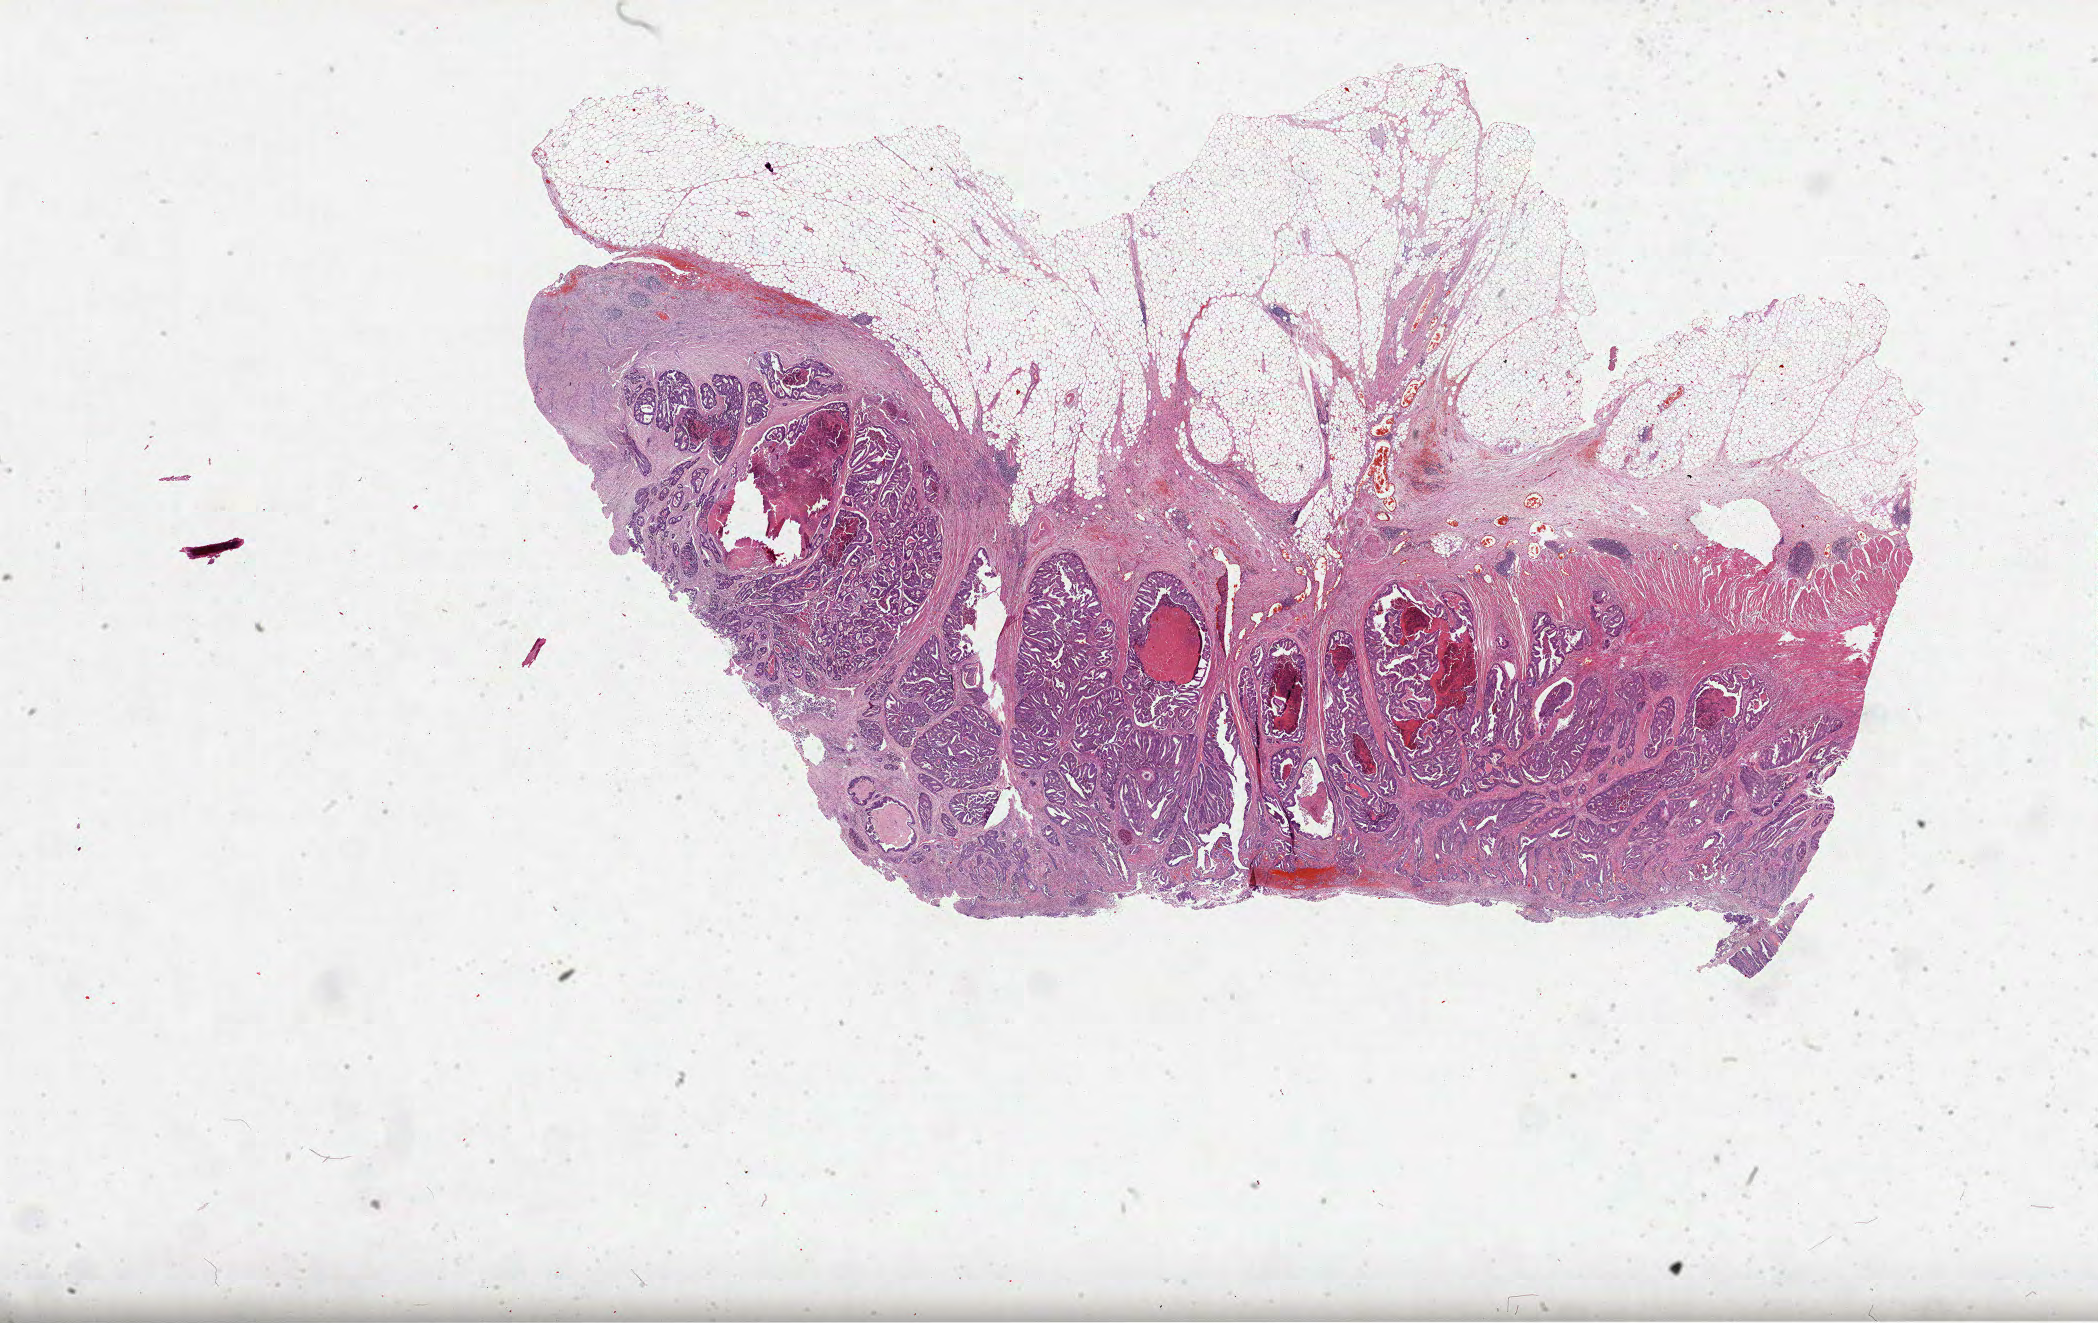
Whole-slide histology image, H&E-stained, shown as a low-resolution overview of the whole scanned area (about 33.8 x 21.3 mm, from a 40x scan). Formalin-fixed paraffin-embedded (FFPE) diagnostic section. Sample: primary tumour, colon. Patient: male, age at initial diagnosis 63 years.
AJCC pathologic stage: IIIB. Lymph nodes positive (case pathology): 1 of 8 examined. Diagnosis: Adenocarcinoma, NOS (sigmoid colon).